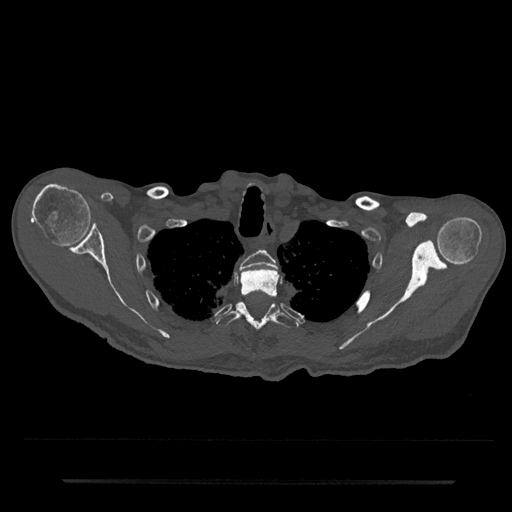
CT including the spine, one axial slice; position 648 of 797 along the scan axis; reconstruction kernel Br40s/3; 120 kVp; bone window (W 1800 / L 400 HU); 0.5 mm slice thickness; 512 × 512 image matrix, field of view 427 × 427 mm. Male patient, age 74 years. From the clinical record (not read from this slice): primary cancer: prostate.
Outlined on this slice (semi-automatically segmented with operator editing):
- T2 vertebra: box from (x=240, y=250) to (x=277, y=270) px
- T3 vertebra: (x=240, y=268)–(x=279, y=298)
- T4 vertebra: (x=216, y=302)–(x=299, y=331)